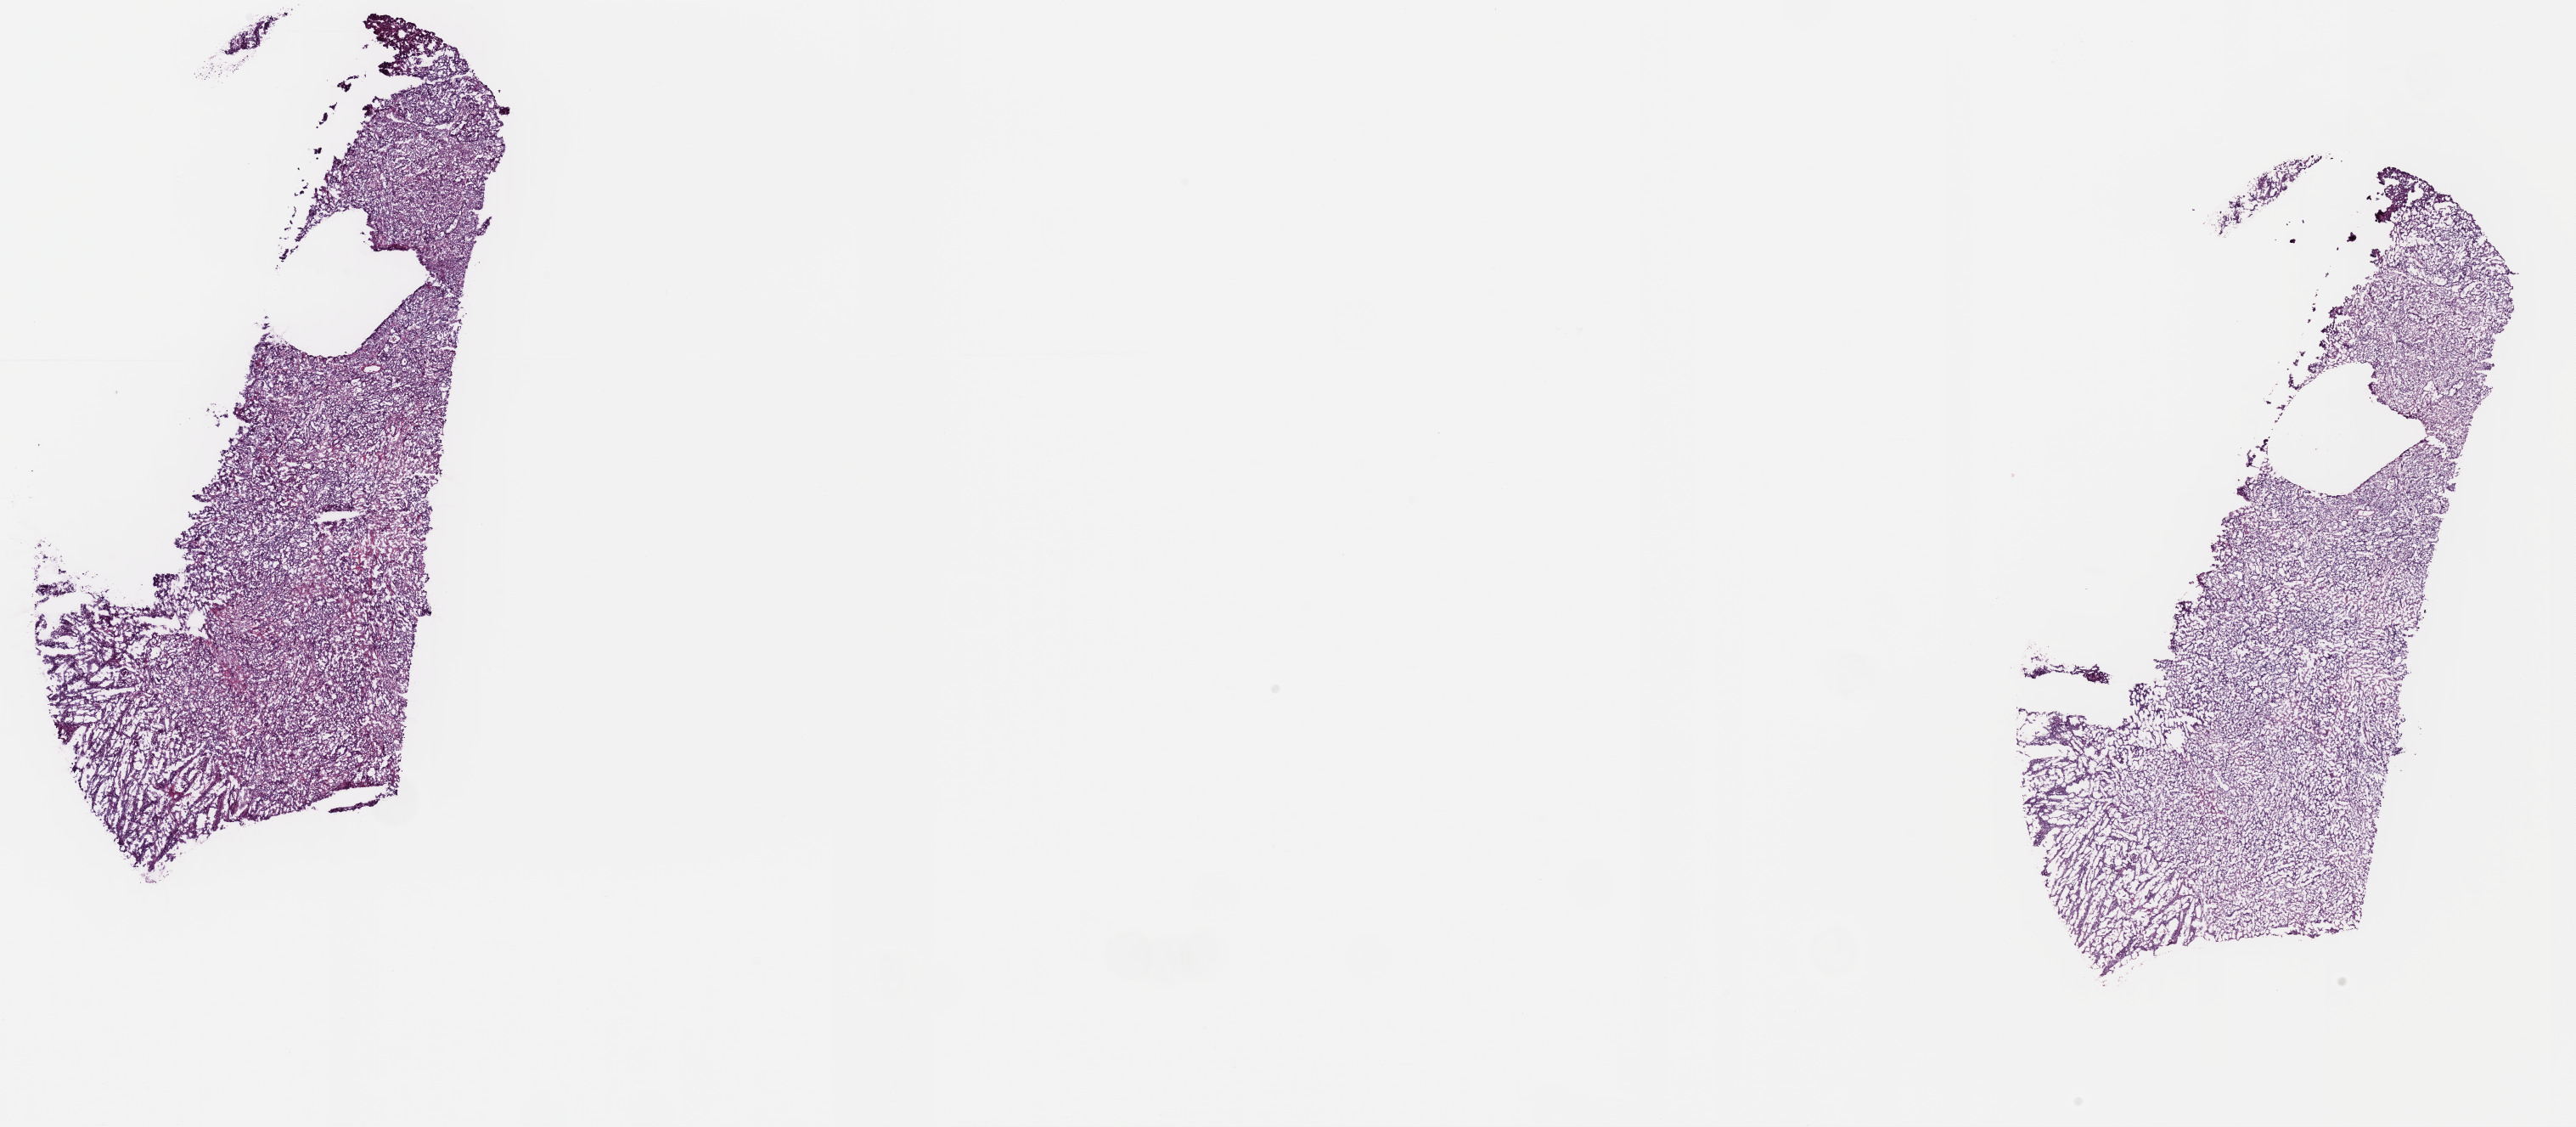
Whole-slide histology image, H&E-stained, whole scanned area (about 24.0 x 10.5 mm) shown as a low-resolution overview. Frozen section from the top of the tissue portion. Uterus, primary tumour sample. Patient: female, age at initial diagnosis 51 years. Histologic grade: G3 (poorly differentiated). Composition of this section per pathologist review: tumour cells 90%, tumour nuclei 90%, normal cells 0%, stromal cells 5%, necrosis 5%. Infiltration values recorded for this section: lymphocyte infiltration 70%, monocyte infiltration 10%, neutrophil infiltration 10%.
FIGO stage: IIIC1. Pathologic diagnosis: Endometrioid adenocarcinoma, NOS (endometrium).